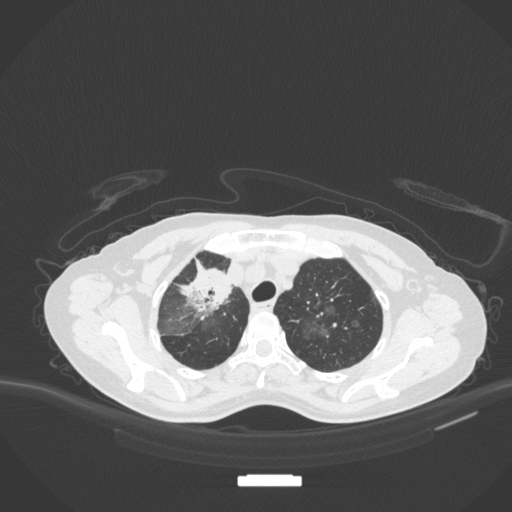
Chest CT, one axial slice; position 264 of 311 along the scan axis; 120 kVp; lung window (W 1500 / L -600 HU); 1 mm slice thickness; 512 × 512 image matrix, field of view 400 × 400 mm. Patient: female, 59 years. Case-level facts recorded for this patient, not image findings: clinical TNM (as recorded): T3 N0 M0; histopathological grade: G1.
Structures marked on this image (bounding box drawn by a radiologist):
- lung tumour (recorded histology: adenocarcinoma): bounding box (x1, y1, x2, y2) in pixels: (180, 260, 237, 325)